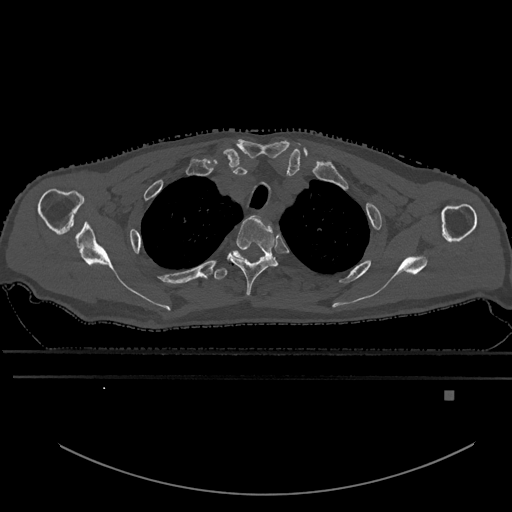
CT including the spine, one axial slice; position 489 of 969 along the scan axis; bone window (W 1800 / L 400 HU); 0.5 mm slice thickness; 512 × 512 image matrix, field of view 456 × 456 mm. Patient: male, 82 years. From the clinical record (not read from this slice): primary cancer: prostate.
Structures marked on this image (semi-automatically segmented with operator editing):
- T2 vertebra: bounding box <227,215,278,297> (left, top, right, bottom; pixels)
- T3 vertebra: <212,251,245,280>